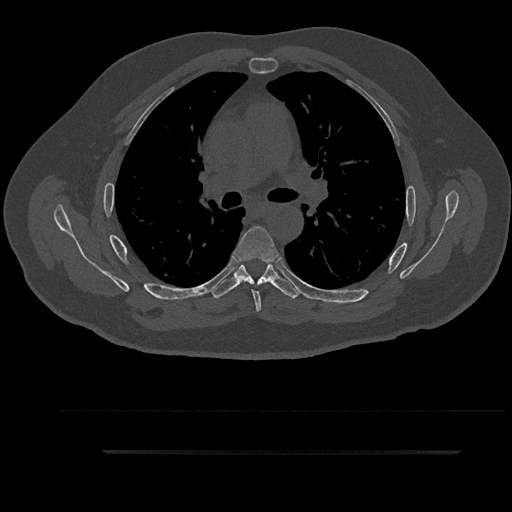
CT including the spine, one axial slice. Reconstruction kernel Br40s/3. 120 kVp. Bone window (W 1800 / L 400 HU). 512 × 512 image matrix, field of view 432 × 432 mm. Male patient, age 63 years. Case-level facts recorded for this patient, not image findings: primary cancer: renal.
Annotated regions visible in this slice (semi-automatically segmented with operator editing):
- T5 vertebra: box from (x=233, y=226) to (x=280, y=312) px
- T6 vertebra: (x=211, y=257)–(x=300, y=298)